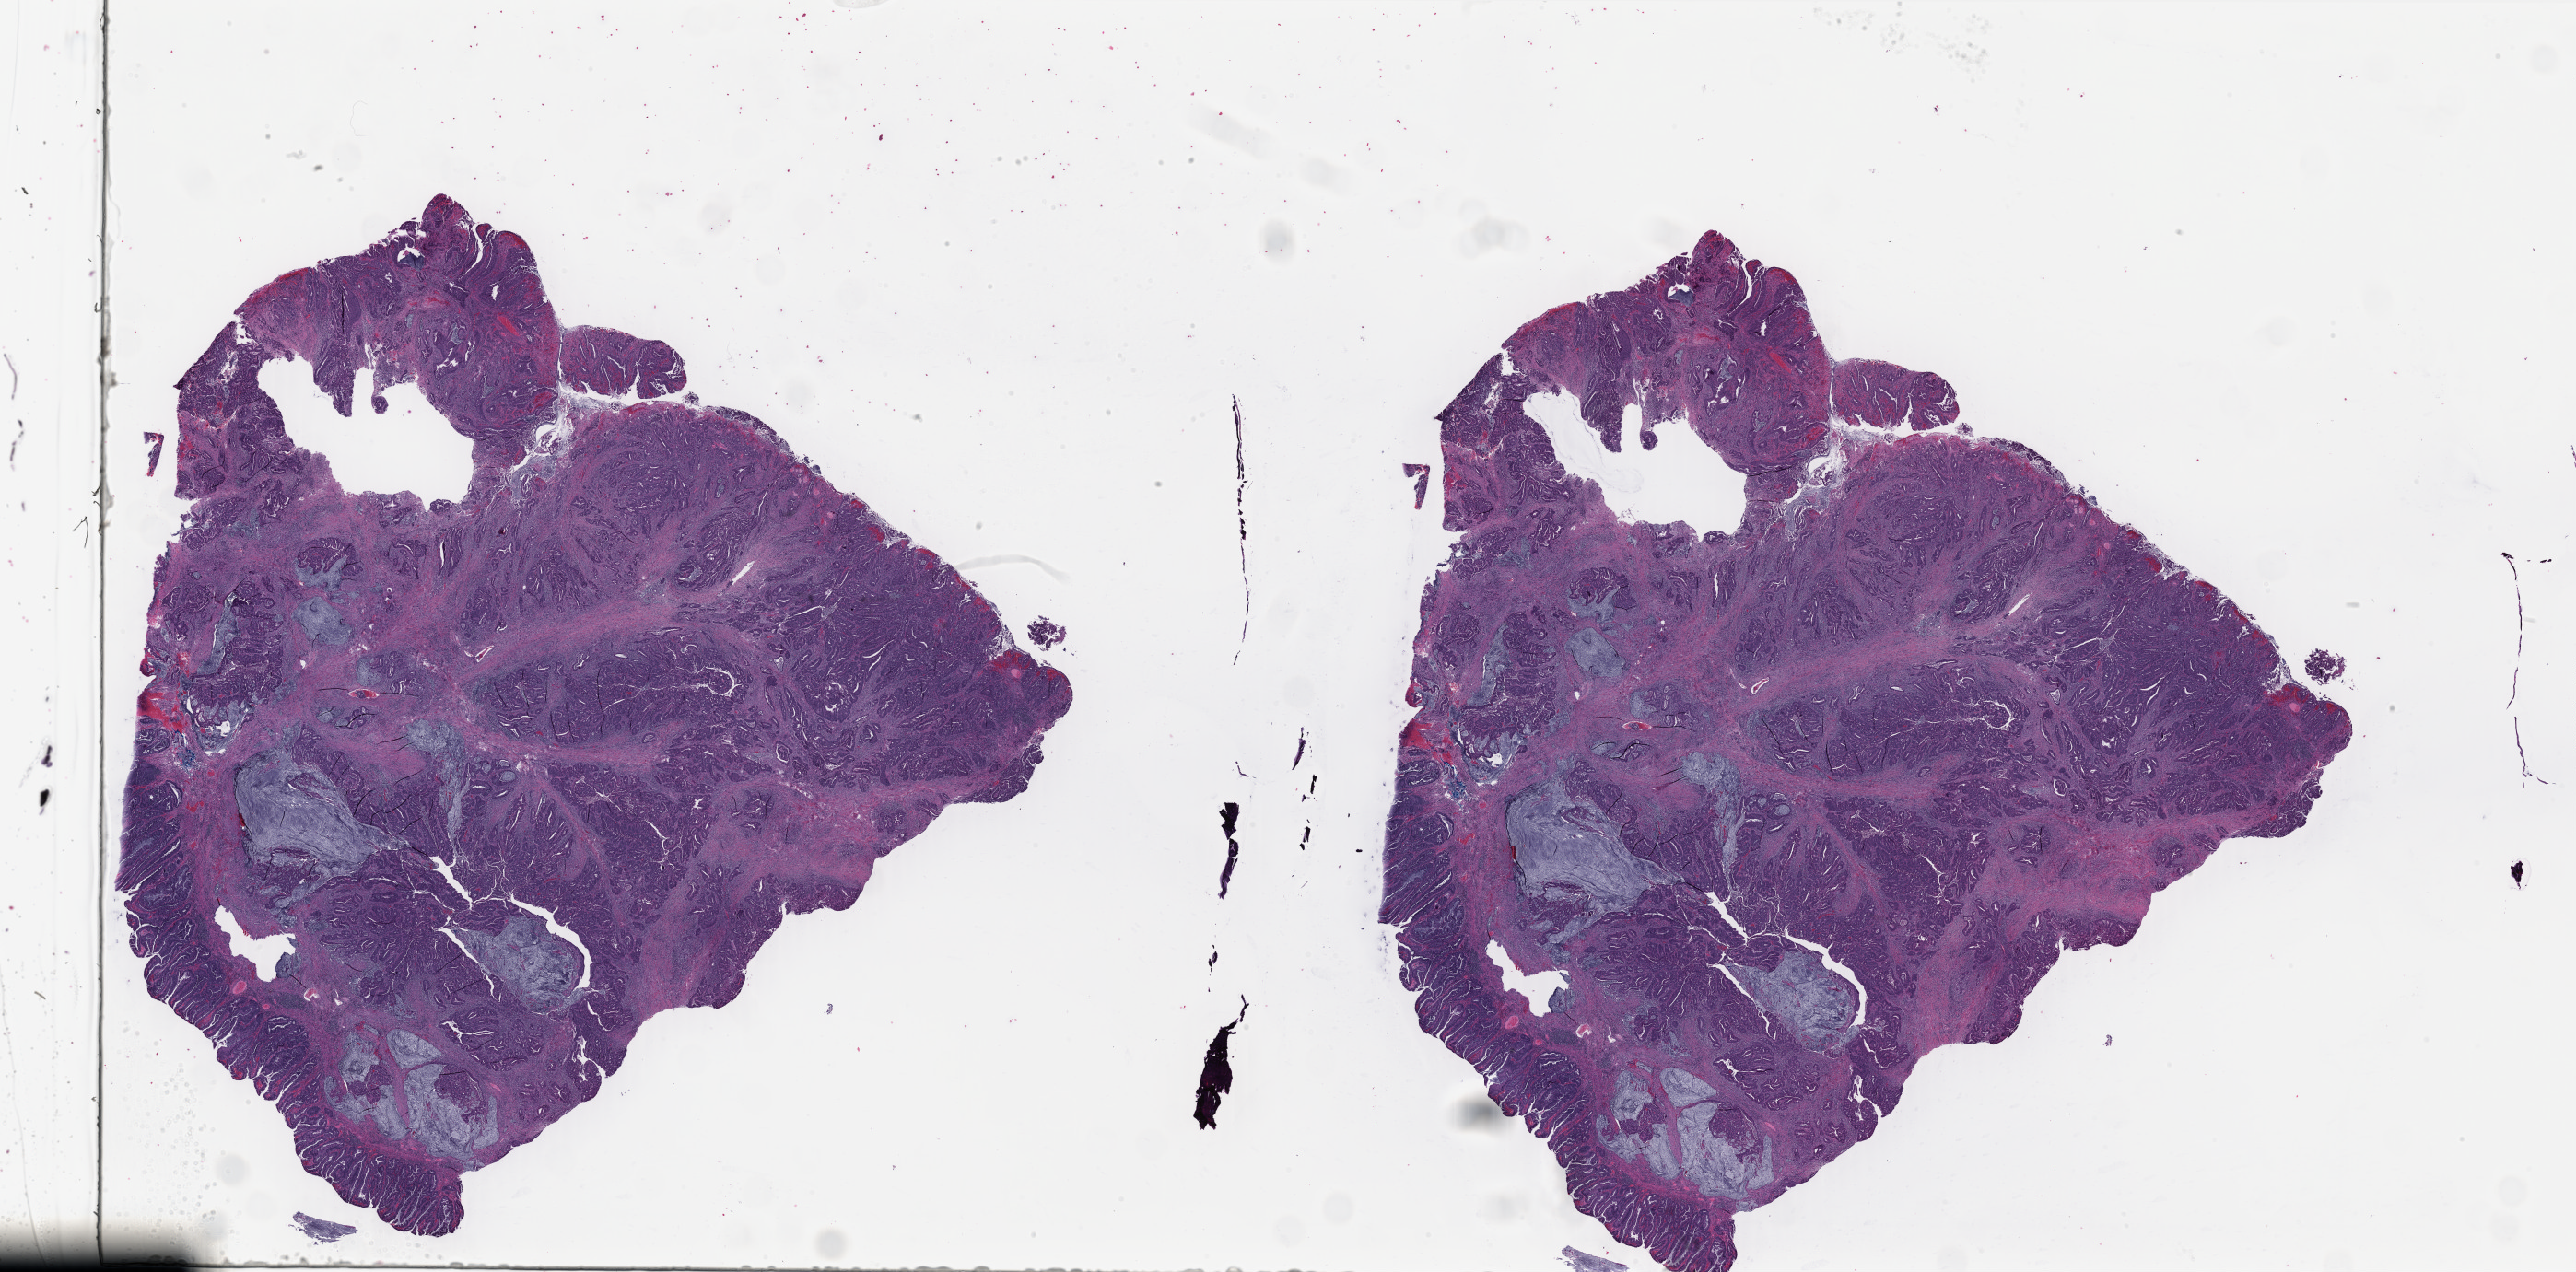
Whole-slide histology image, H&E-stained, shown as a low-resolution overview of the whole scanned area (about 44.2 x 21.9 mm); formalin-fixed paraffin-embedded (FFPE) diagnostic section; primary tumour sample from the colon. Female, age 54 years at initial diagnosis.
Diagnosis: Adenocarcinoma, NOS (cecum).